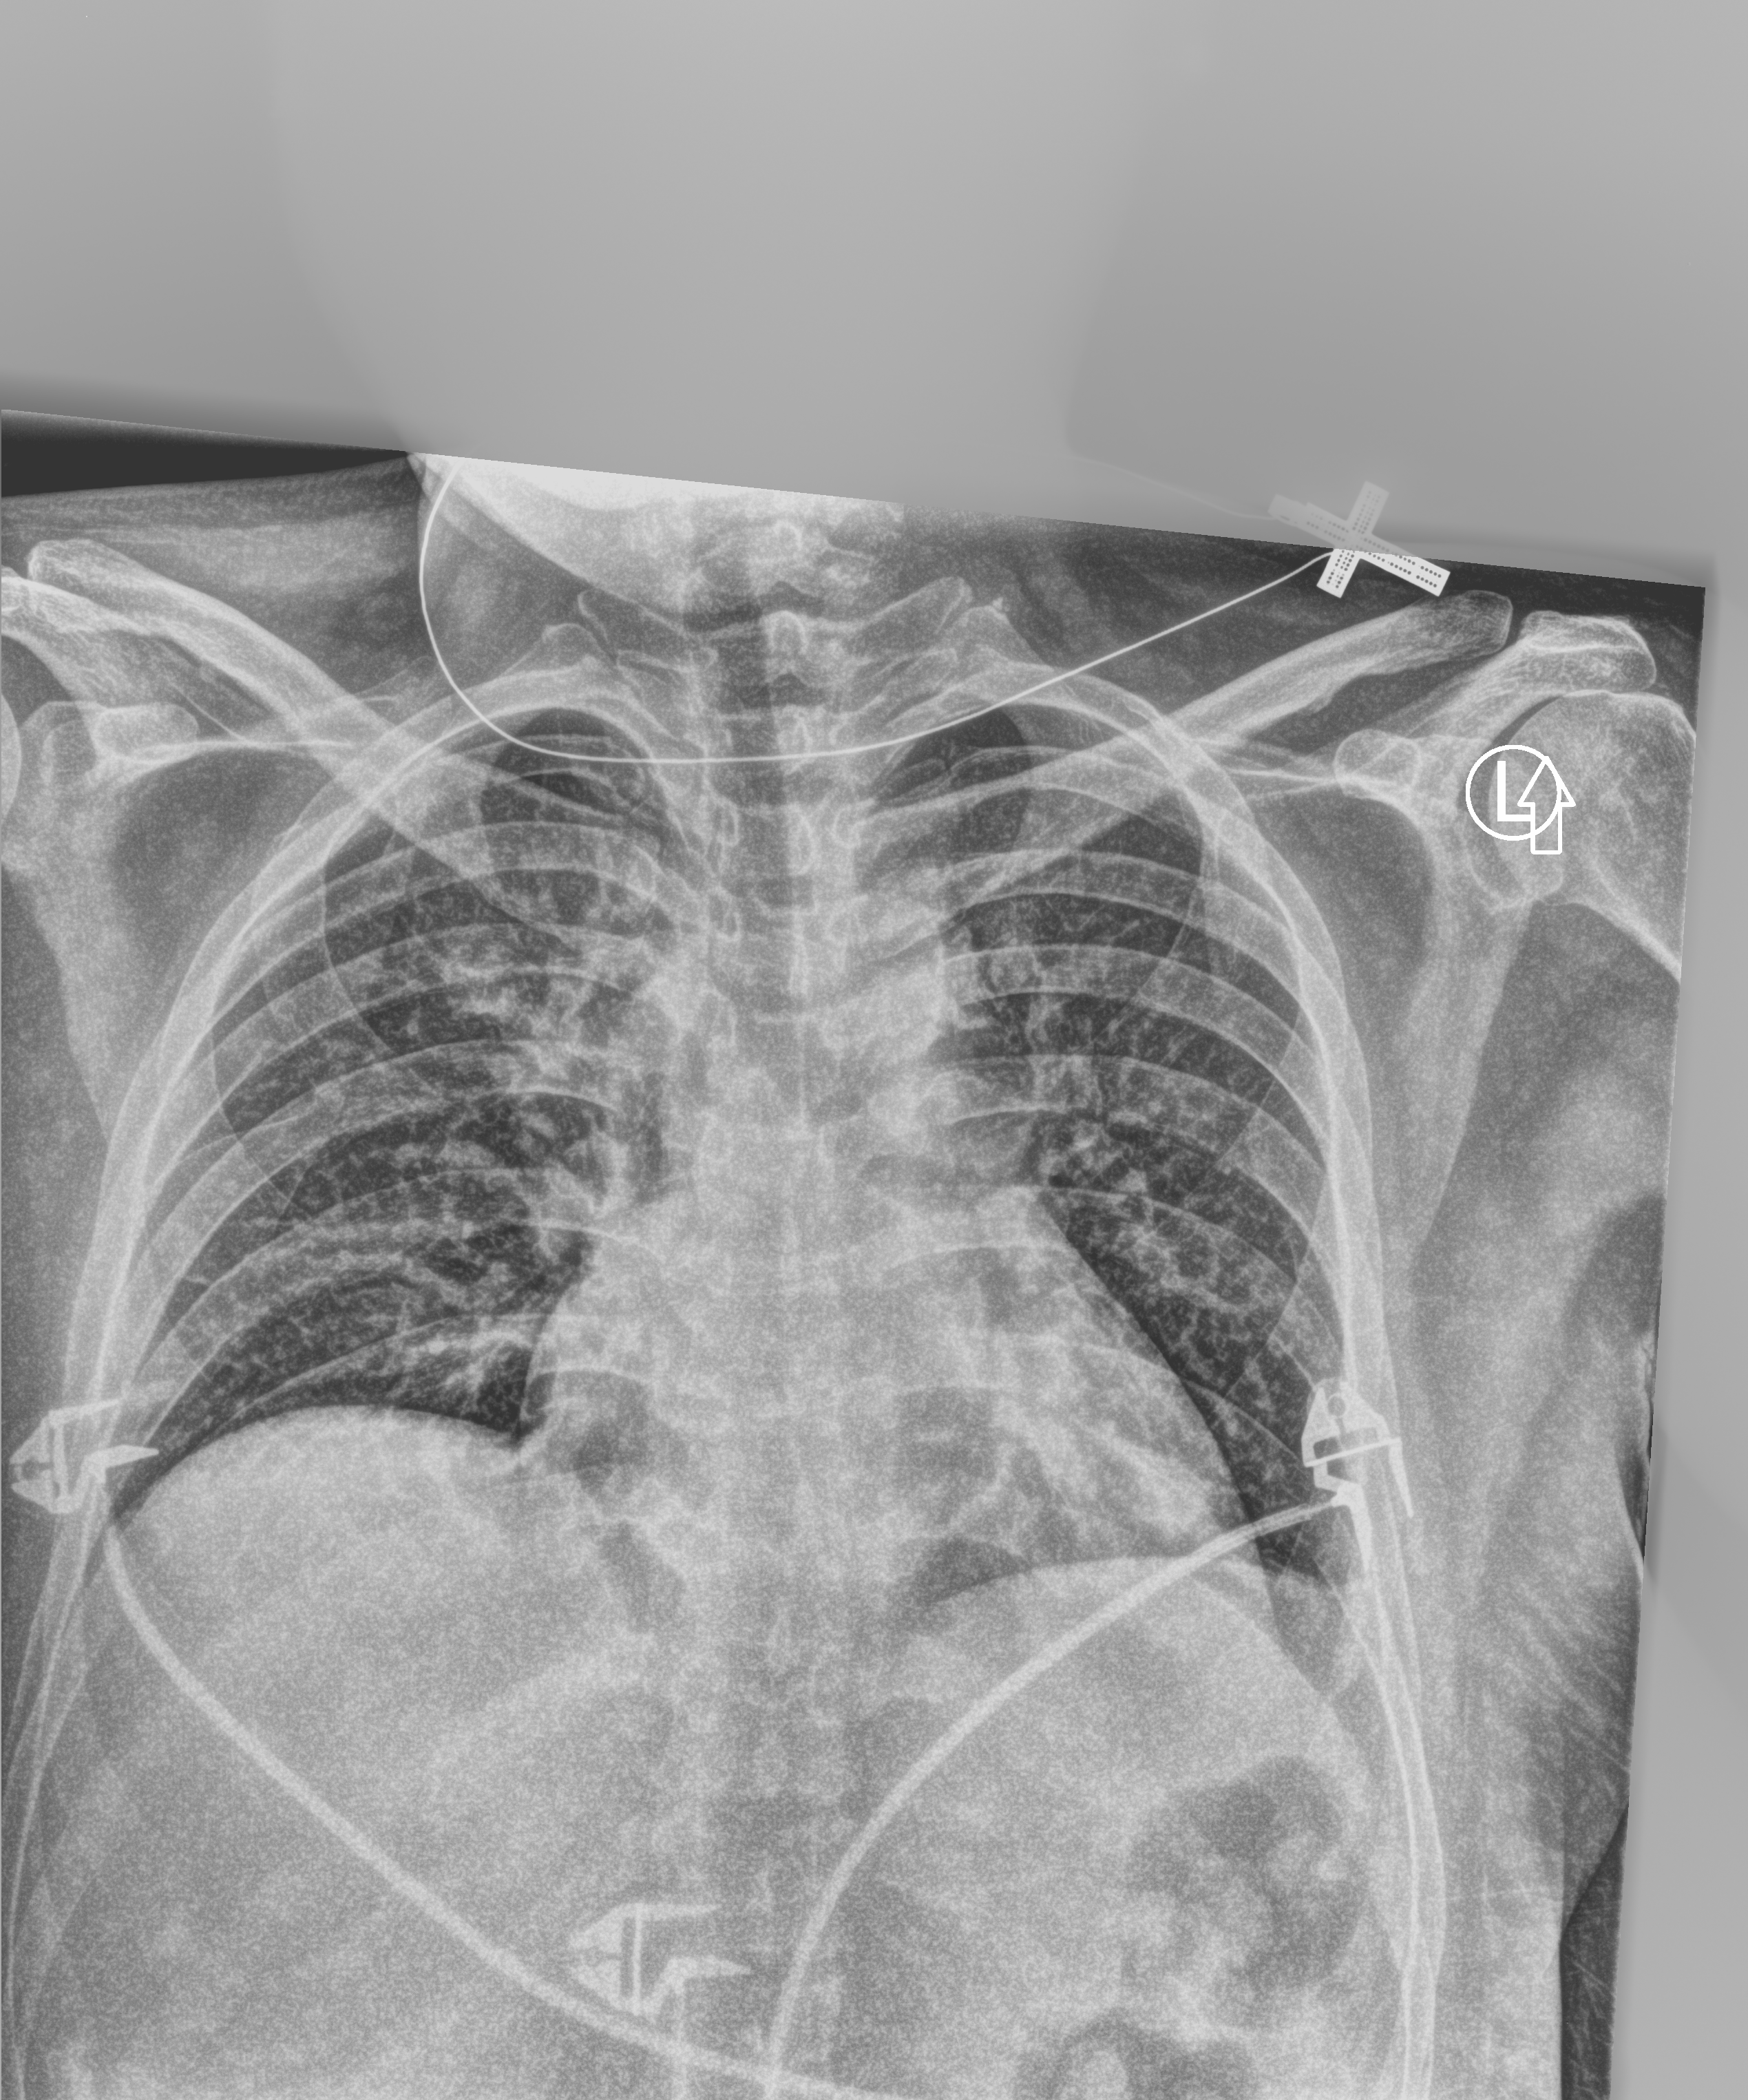
Portable chest radiograph, anteroposterior (AP) projection. Patient hospitalised with COVID-19; female, aged 18–59 years.
Hospital-stay facts (about this admission, not read from this image; timing relative to this image not recorded): length of hospital stay: 10 days; hypertension (admission record): yes; admitted to intensive care during this hospital stay: no.